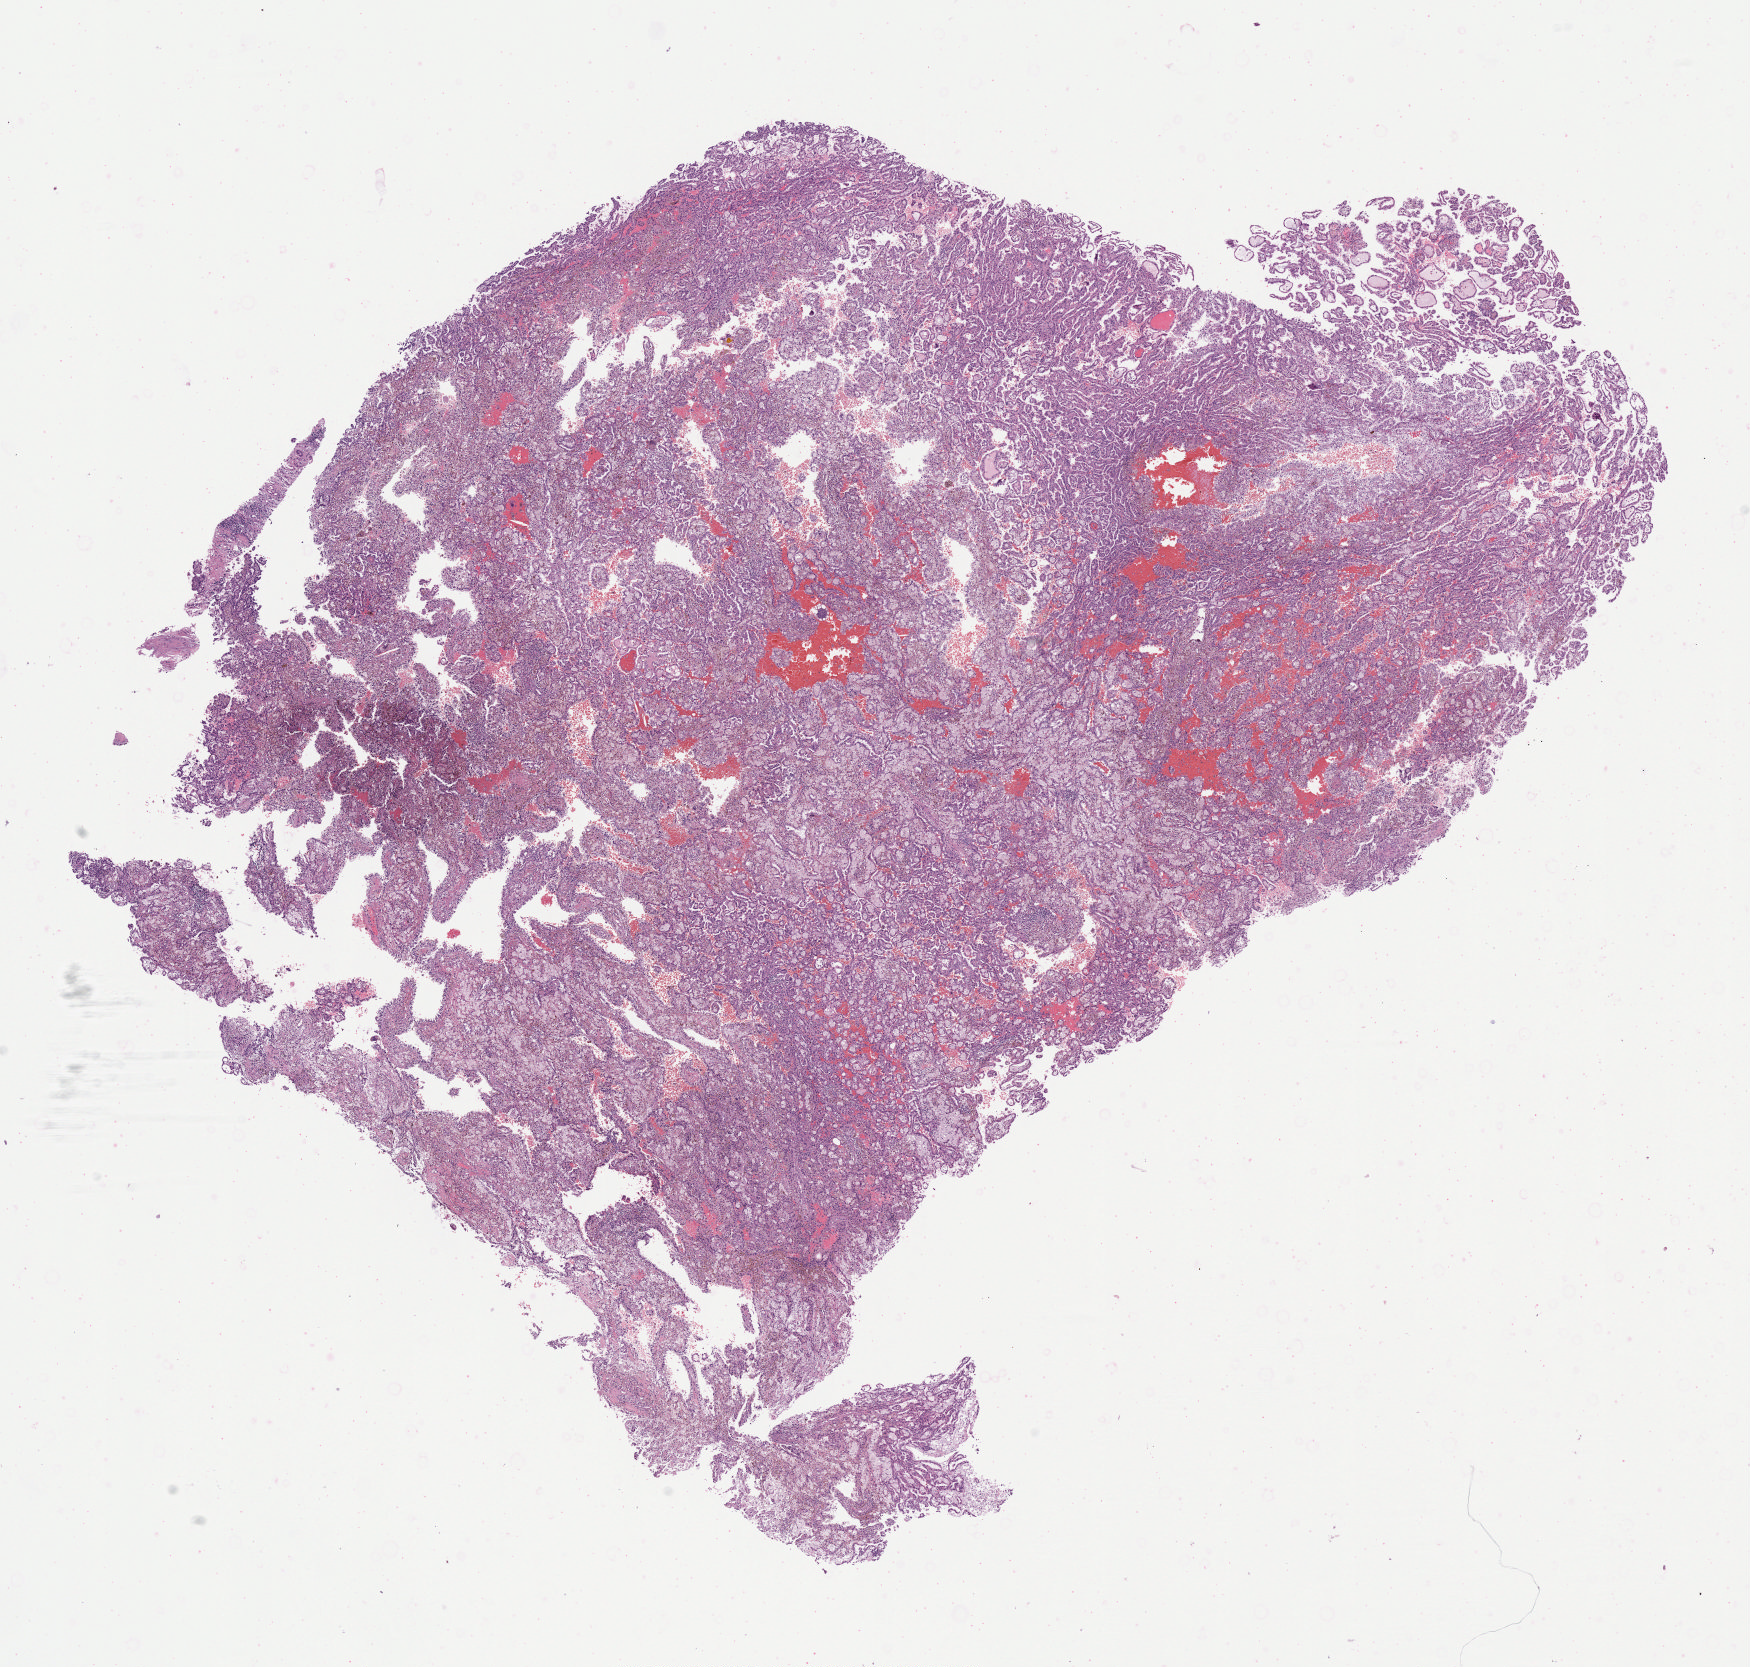
H&E whole-slide image — low-resolution overview of the scanned area, about 14.0 x 13.4 mm; FFPE section; sample: primary tumour, kidney. Male patient; age at initial diagnosis 73 years.
Diagnosis: Papillary adenocarcinoma, NOS. AJCC pathologic stage: I (7th edition). Laterality: left.